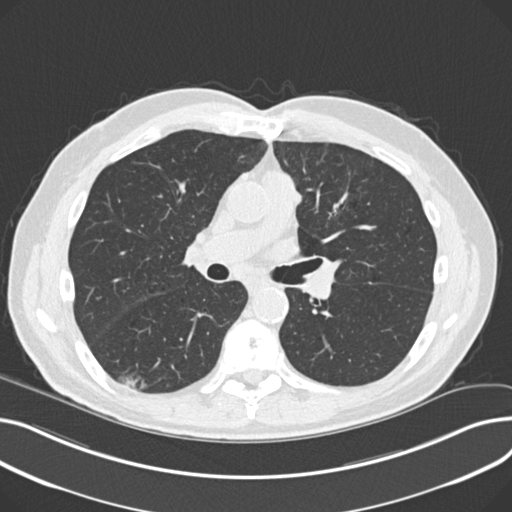
Chest CT (low-dose screening protocol), one axial image. Third screening round (two years after baseline). Lung window (W 1500 / L -600 HU). 2 mm slice thickness. 120 kVp. Slice 107 of 230 in the series. 512 × 512 image matrix, field of view 372 × 372 mm. Male participant, aged 68 years at enrolment. Current smoker at enrolment.
Expert-annotated lung lesion, bounding box [x1, y1, x2, y2] px = [122, 366, 160, 398]. The screening reader recorded 5 non-calcified nodules or masses ≥4 mm on this exam (right upper lobe, left upper lobe, right upper lobe, right lower lobe, right upper lobe); which of them this box marks is not recorded.